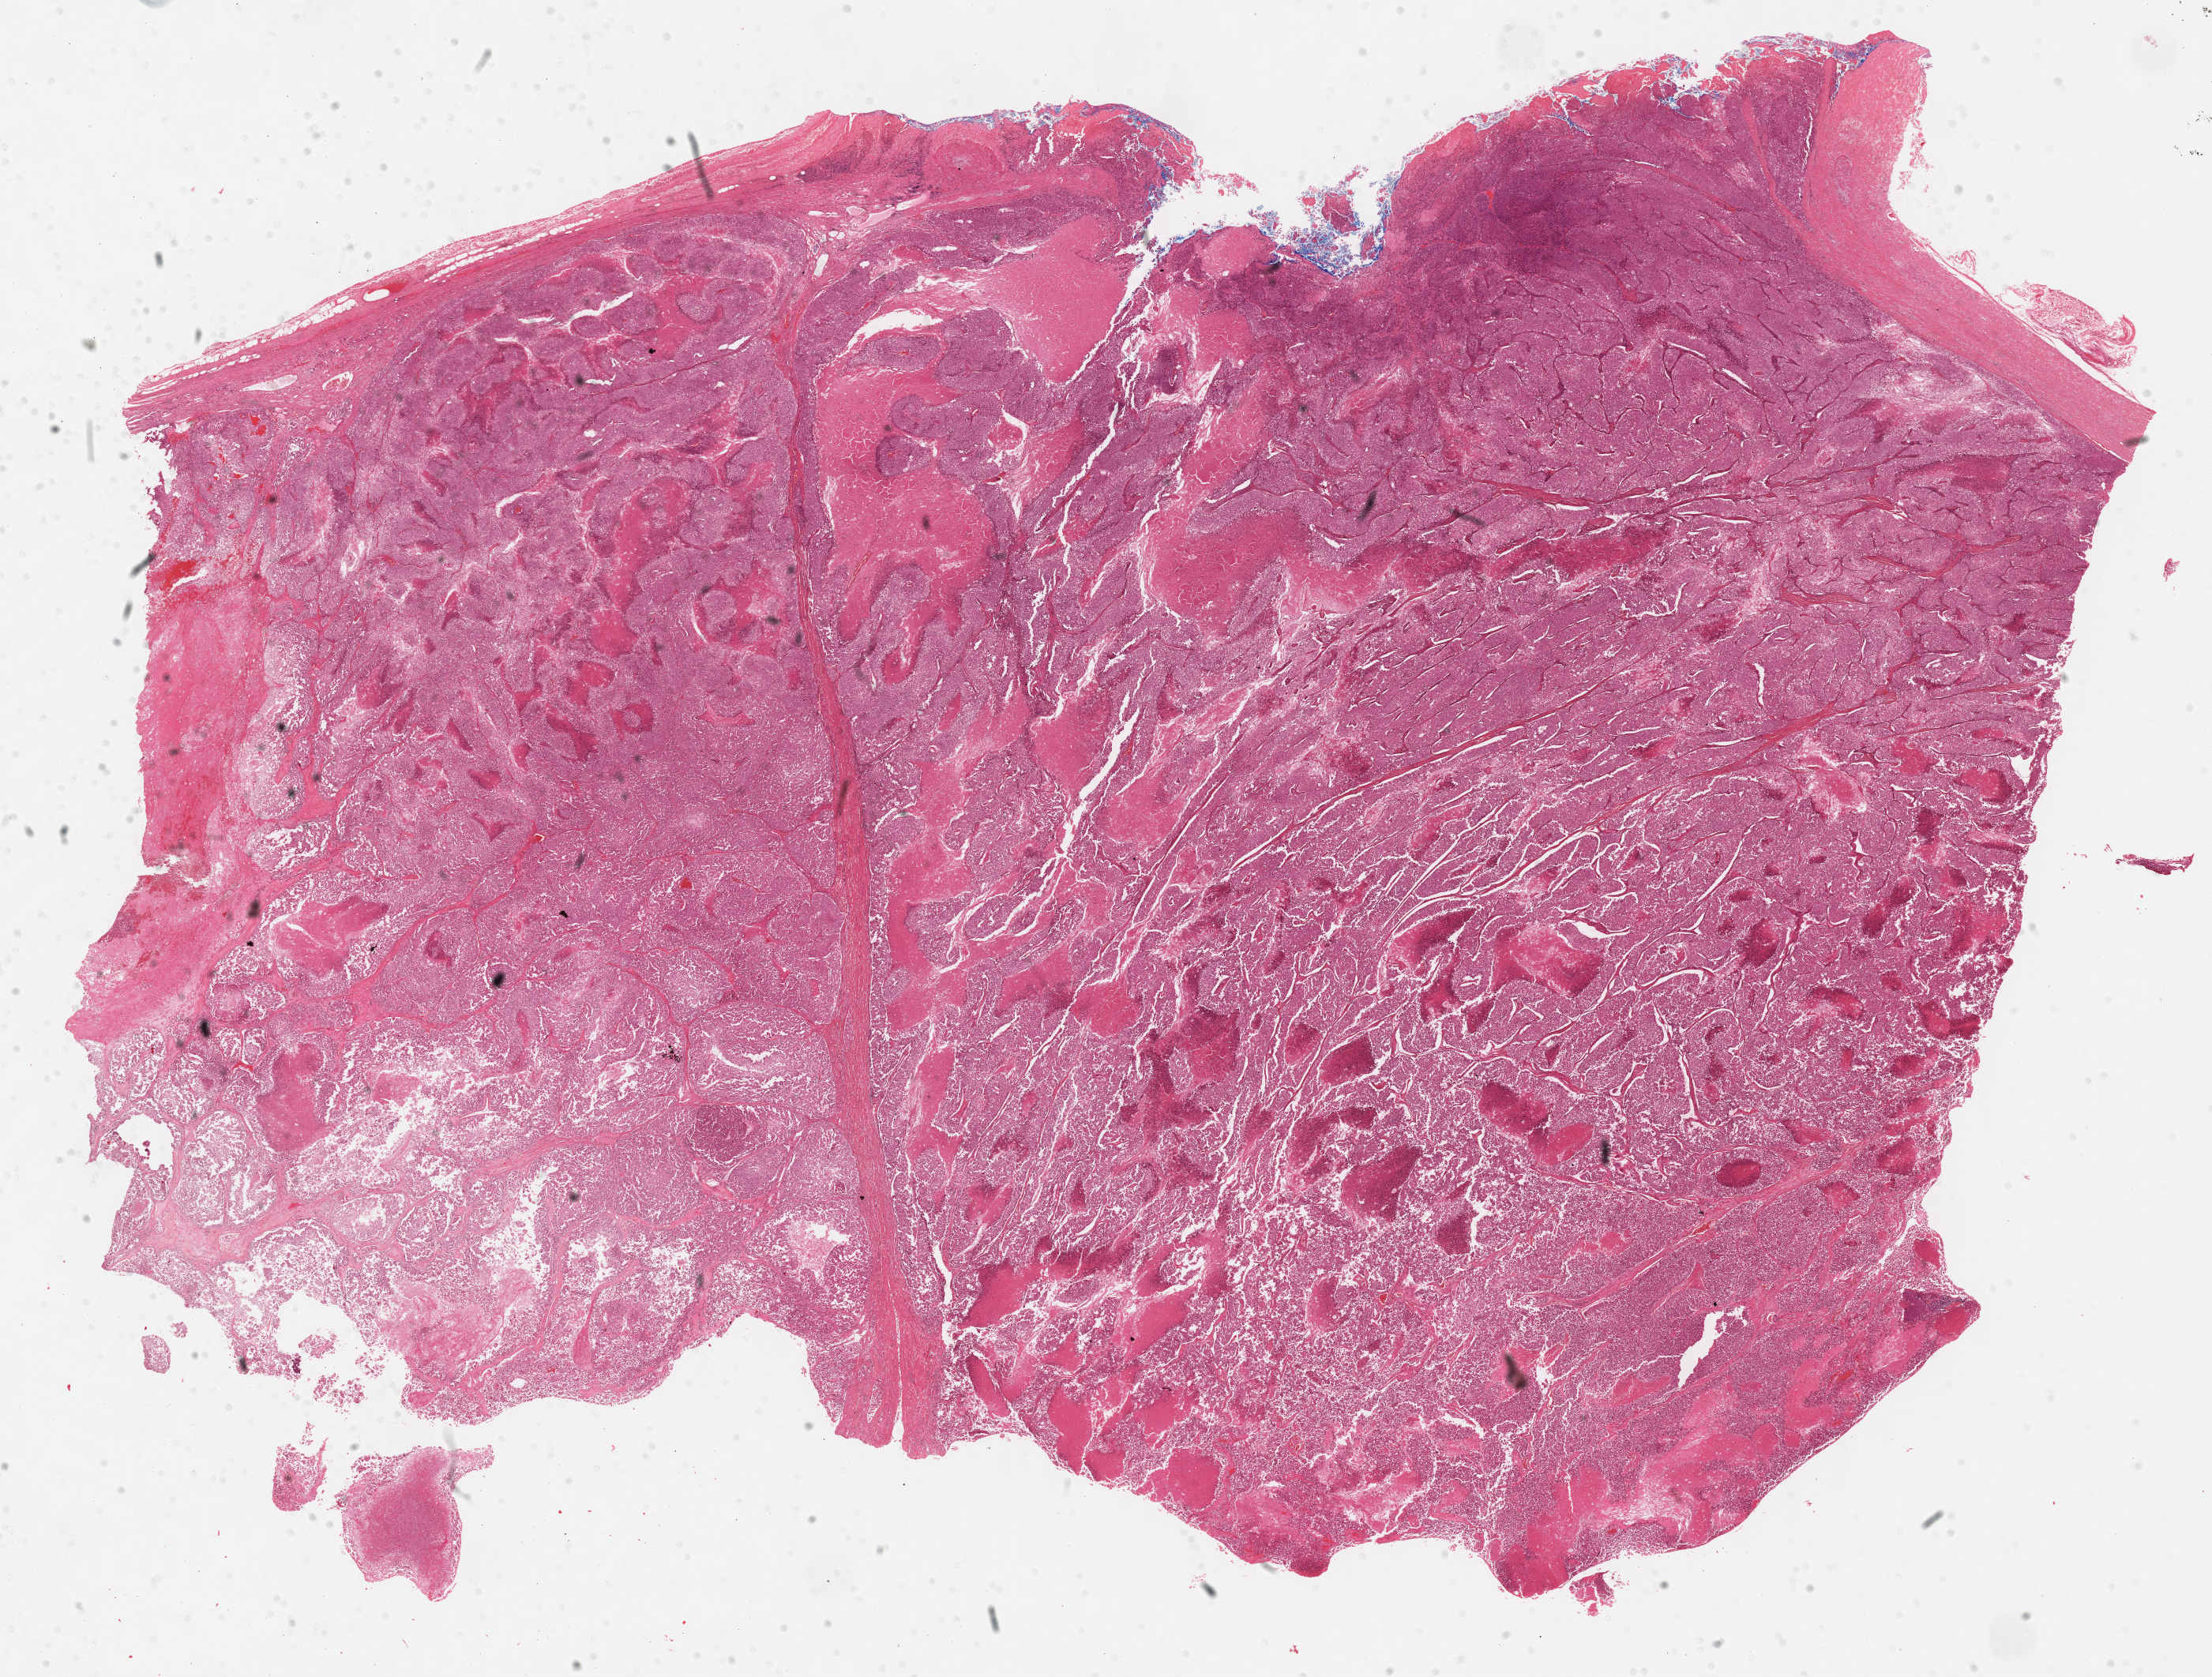
H&E whole-slide image — a low-resolution overview of the entire scanned area, about 22.7 x 17.2 mm (acquisition: 40x scan). Formalin-fixed paraffin-embedded (FFPE) diagnostic section. Adrenal cortex, primary tumour sample. Patient: male, age at initial diagnosis 65 years.
* diagnosis: Adrenal cortical carcinoma
* lymph nodes positive (case pathology): 6 of 6 examined